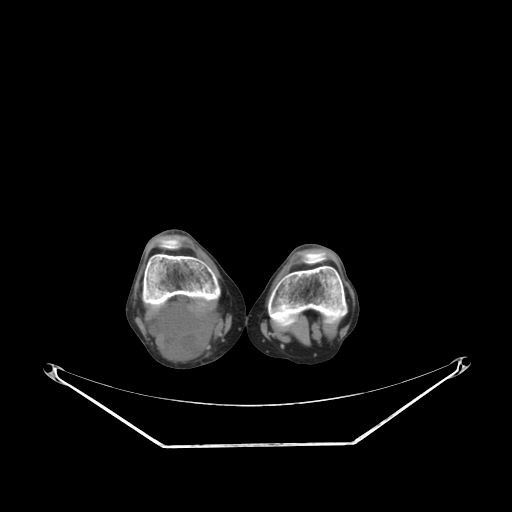
CT of an extremity soft-tissue mass (from a PET/CT study), one axial slice. Slice 171 of 267 in the series (ordered by position). Soft-tissue window (W 400 / L 40 HU). 3.75 mm slice thickness. 512 × 512 image matrix. Female patient. Case-level facts recorded for this patient, not image findings: histological type: liposarcoma; site of the primary tumour: right thigh.
Annotated regions visible in this slice (expert contour drawn on MRI and transferred to this co-registered scan by the dataset authors):
- gross tumour volume (mass): bounding box (x1, y1, x2, y2) in pixels: (149, 301, 220, 362)